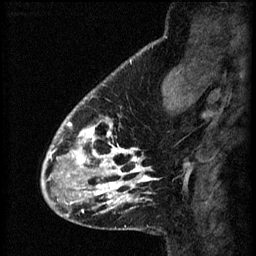
Breast MRI (dynamic contrast-enhanced), one sagittal slice; position 16 of 60 along the scan axis; 3 images stored at this slice position (order not interpretable as contrast timing); 1.5 T; TE 4.2 ms, TR 8.2 ms; 256 × 256 image matrix, field of view 180 × 180 mm. Female patient, age 41 years.
Structures marked on this image (semi-automatically segmented with operator editing):
- analysis volume of interest (the breast-tissue region the enhancement analysis was run in; not a lesion): box from (x=56, y=104) to (x=157, y=207) px
- tumour enhancement mask (voxels above the 70 % enhancement threshold inside the analysis volume of interest): (x=56, y=108)–(x=157, y=207)